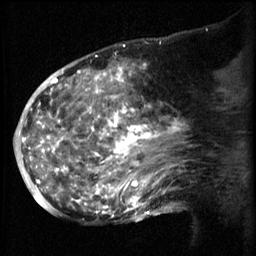
Breast MRI (dynamic contrast-enhanced), one sagittal slice; slice 32 of 60 in the series (ordered by position); 3 images stored at this slice position (order not interpretable as contrast timing); 1.5 T; TE 4.2 ms, TR 8.2 ms; 2.3 mm slice thickness; 256 × 256 image matrix, field of view 200 × 200 mm. Patient: female, 50 years.
Outlined on this slice (semi-automatic segmentation, software-assisted and operator-edited):
- analysis volume of interest (the breast-tissue region the enhancement analysis was run in; not a lesion): bounding box <50,64,169,217> (left, top, right, bottom; pixels)
- tumour enhancement mask (voxels above the 70 % enhancement threshold inside the analysis volume of interest): <50,64,165,217>